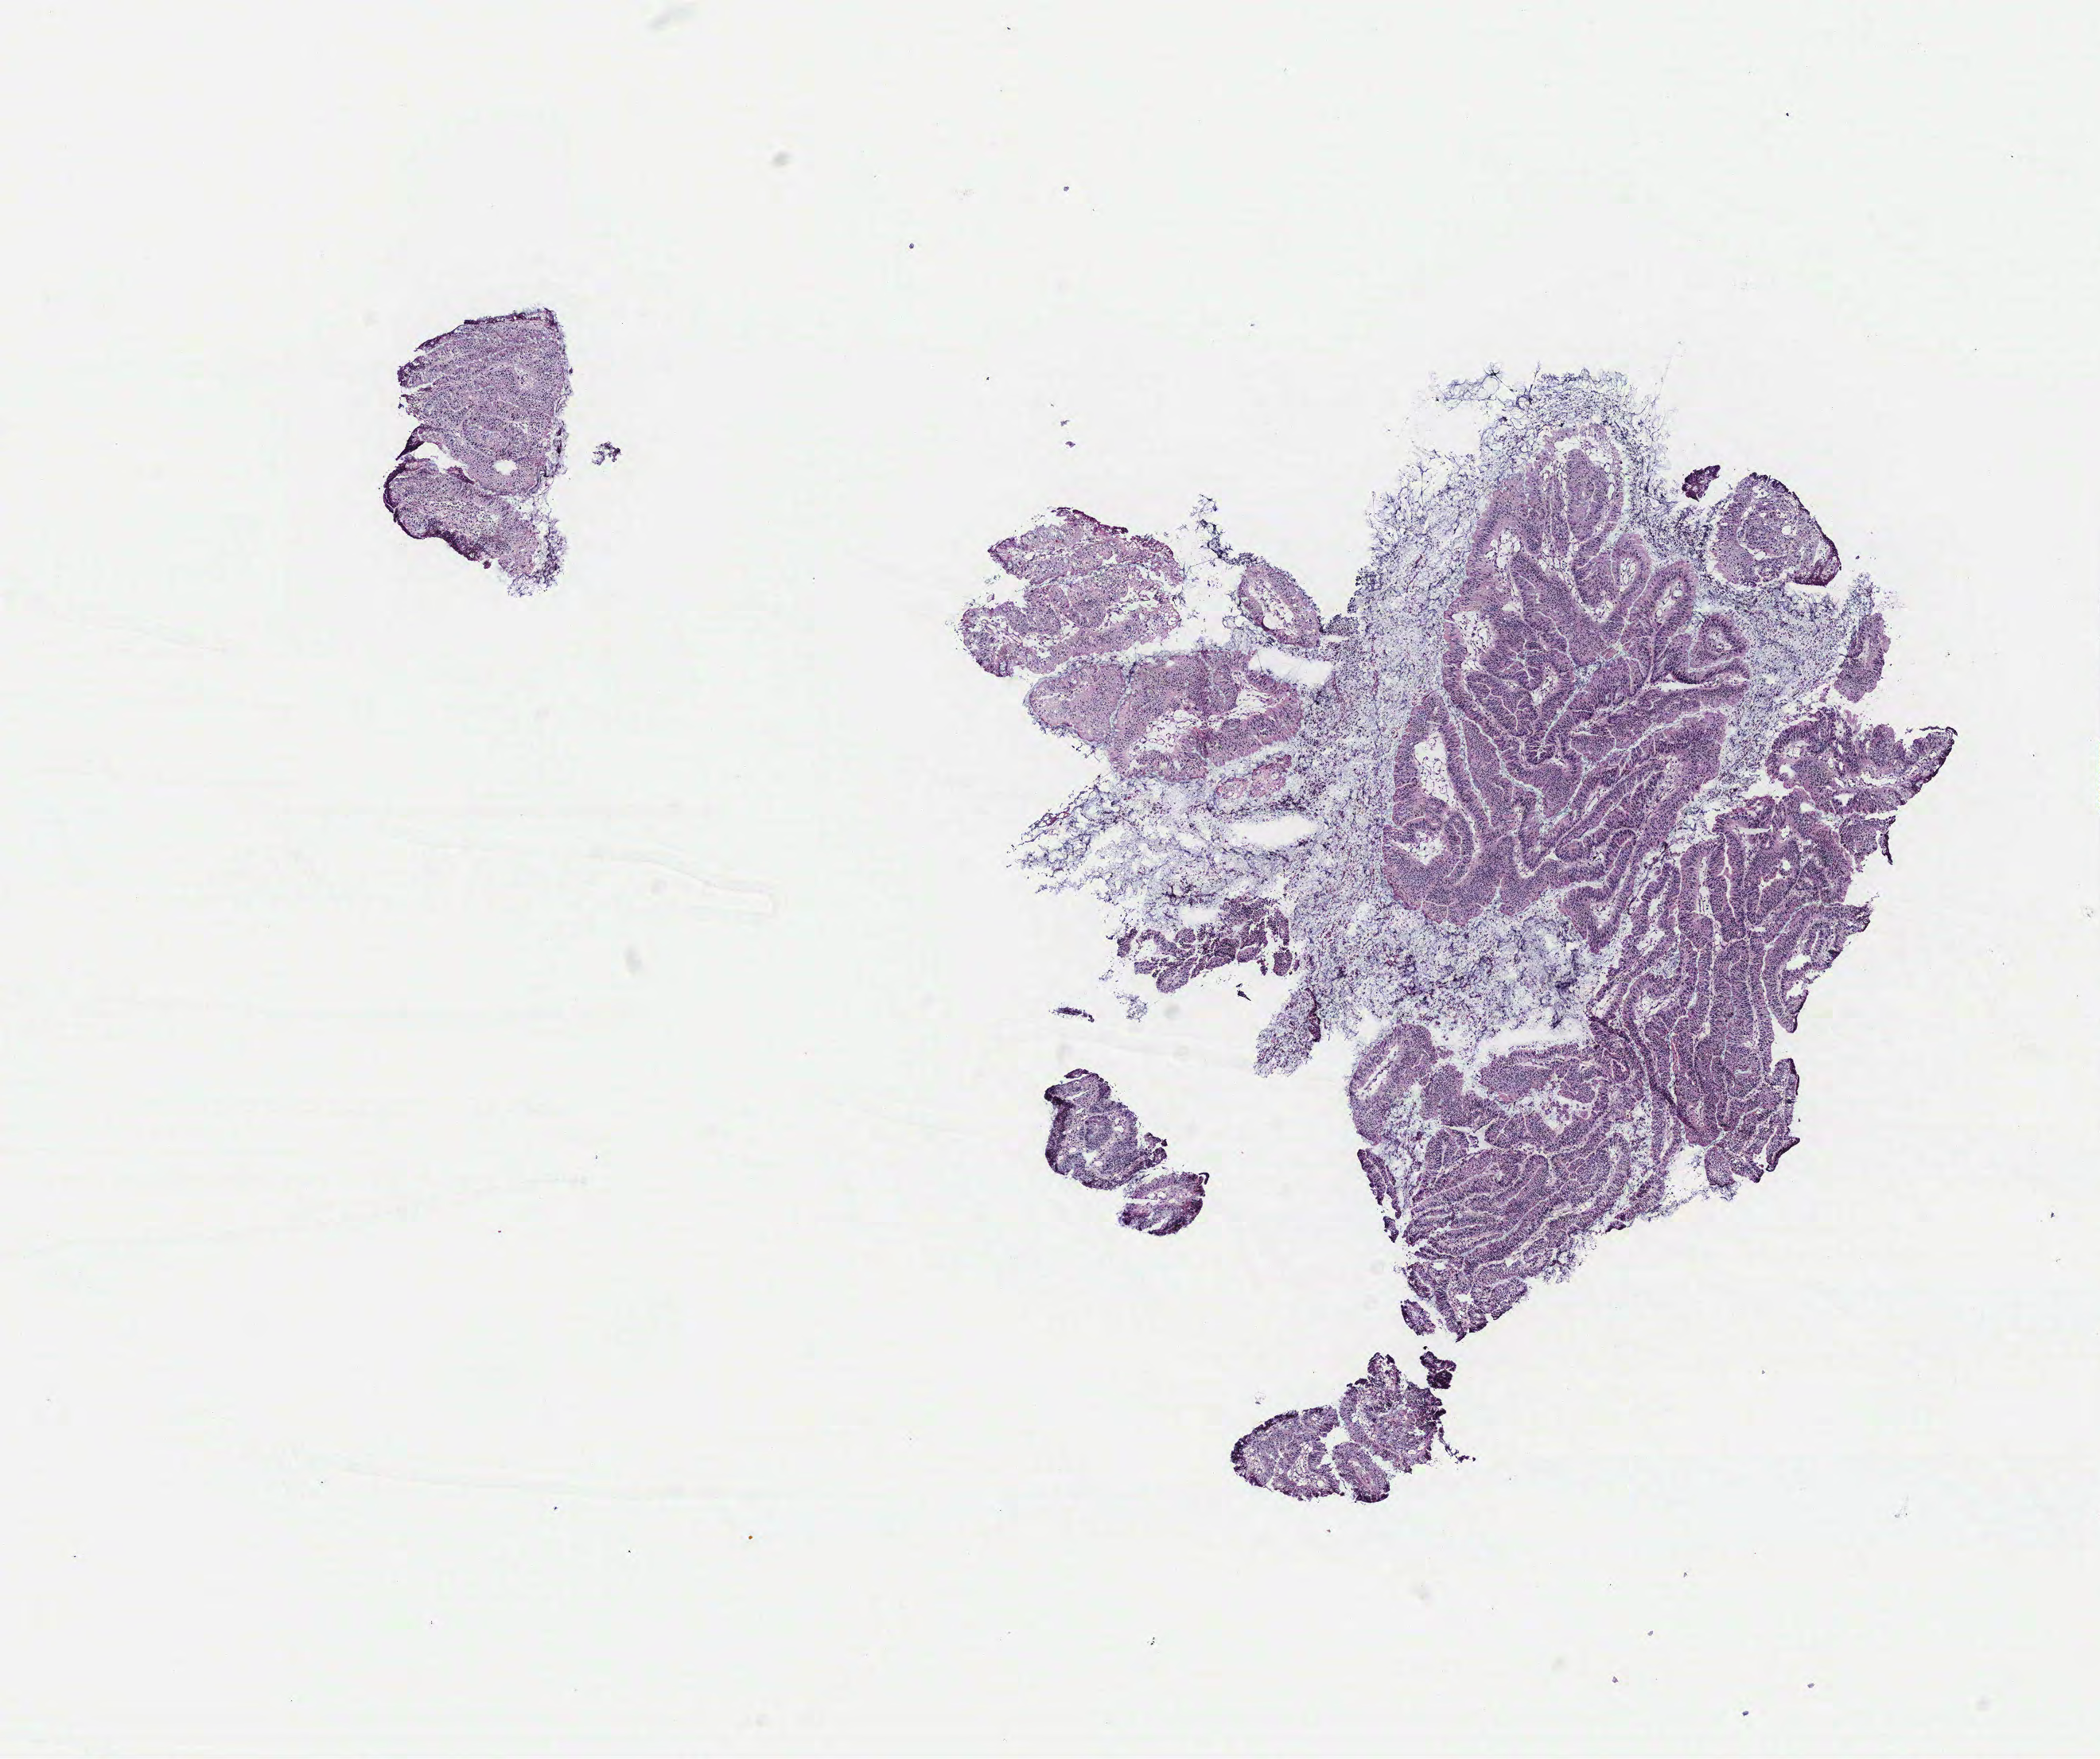
H&E-stained whole-slide image, shown as a low-resolution overview of the whole scanned area (about 10.6 x 8.8 mm, slide scanned at 40x); colon, tissue type not recorded.
Patient diagnosis (cohort enrolment): colon cancer (colon).